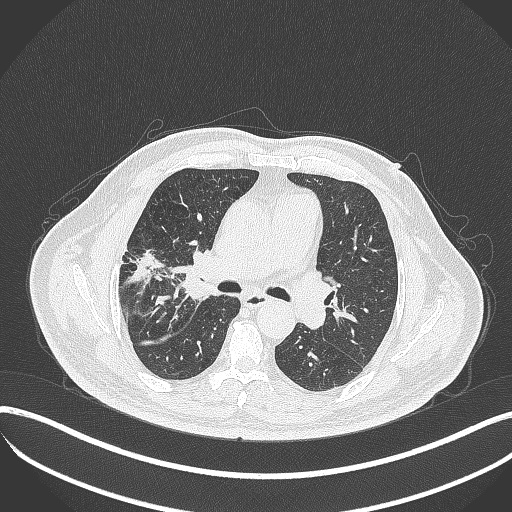
Chest CT, one axial slice. Position 215 of 401 along the scan axis. Reconstruction kernel B70f. 120 kVp. Lung window (W 1500 / L -600 HU). 512 × 512 image matrix, field of view 400 × 400 mm. Patient: male, 72 years. From the clinical record (not read from this slice): clinical TNM (as recorded): T1c N0 M0; histopathological grade: G2.
Structures marked on this image (bounding box drawn by a radiologist):
- lung tumour (recorded histology: squamous cell carcinoma): bounding box (x1, y1, x2, y2) in pixels: (163, 241, 209, 307)